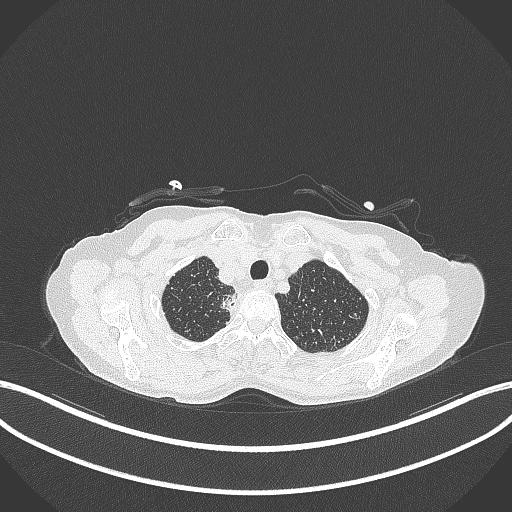
Chest CT, one axial slice; slice 332 of 403 in the series (ordered by position); 120 kVp; lung window (W 1500 / L -600 HU); 1 mm slice thickness; 512 × 512 image matrix, field of view 400 × 400 mm. Female patient, age 75 years. From the clinical record (not read from this slice): clinical TNM (as recorded): T1c N1 M1.
Structures marked on this image (bounding box drawn by a radiologist):
- lung tumour (recorded histology: adenocarcinoma): bounding box [x1, y1, x2, y2] px = [216, 289, 240, 315]